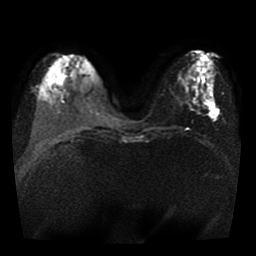
Breast MRI, one axial slice; position 14 of 41 along the scan axis; diffusion-weighted series; image 2 of 4 stored at this slice position (different b-values; order by instance number); 1.5 T; 256 × 256 image matrix. Female patient.
Annotated regions visible in this slice (outlined manually by an expert reader):
- tumour on diffusion-weighted imaging: box from (x=210, y=104) to (x=219, y=118) px